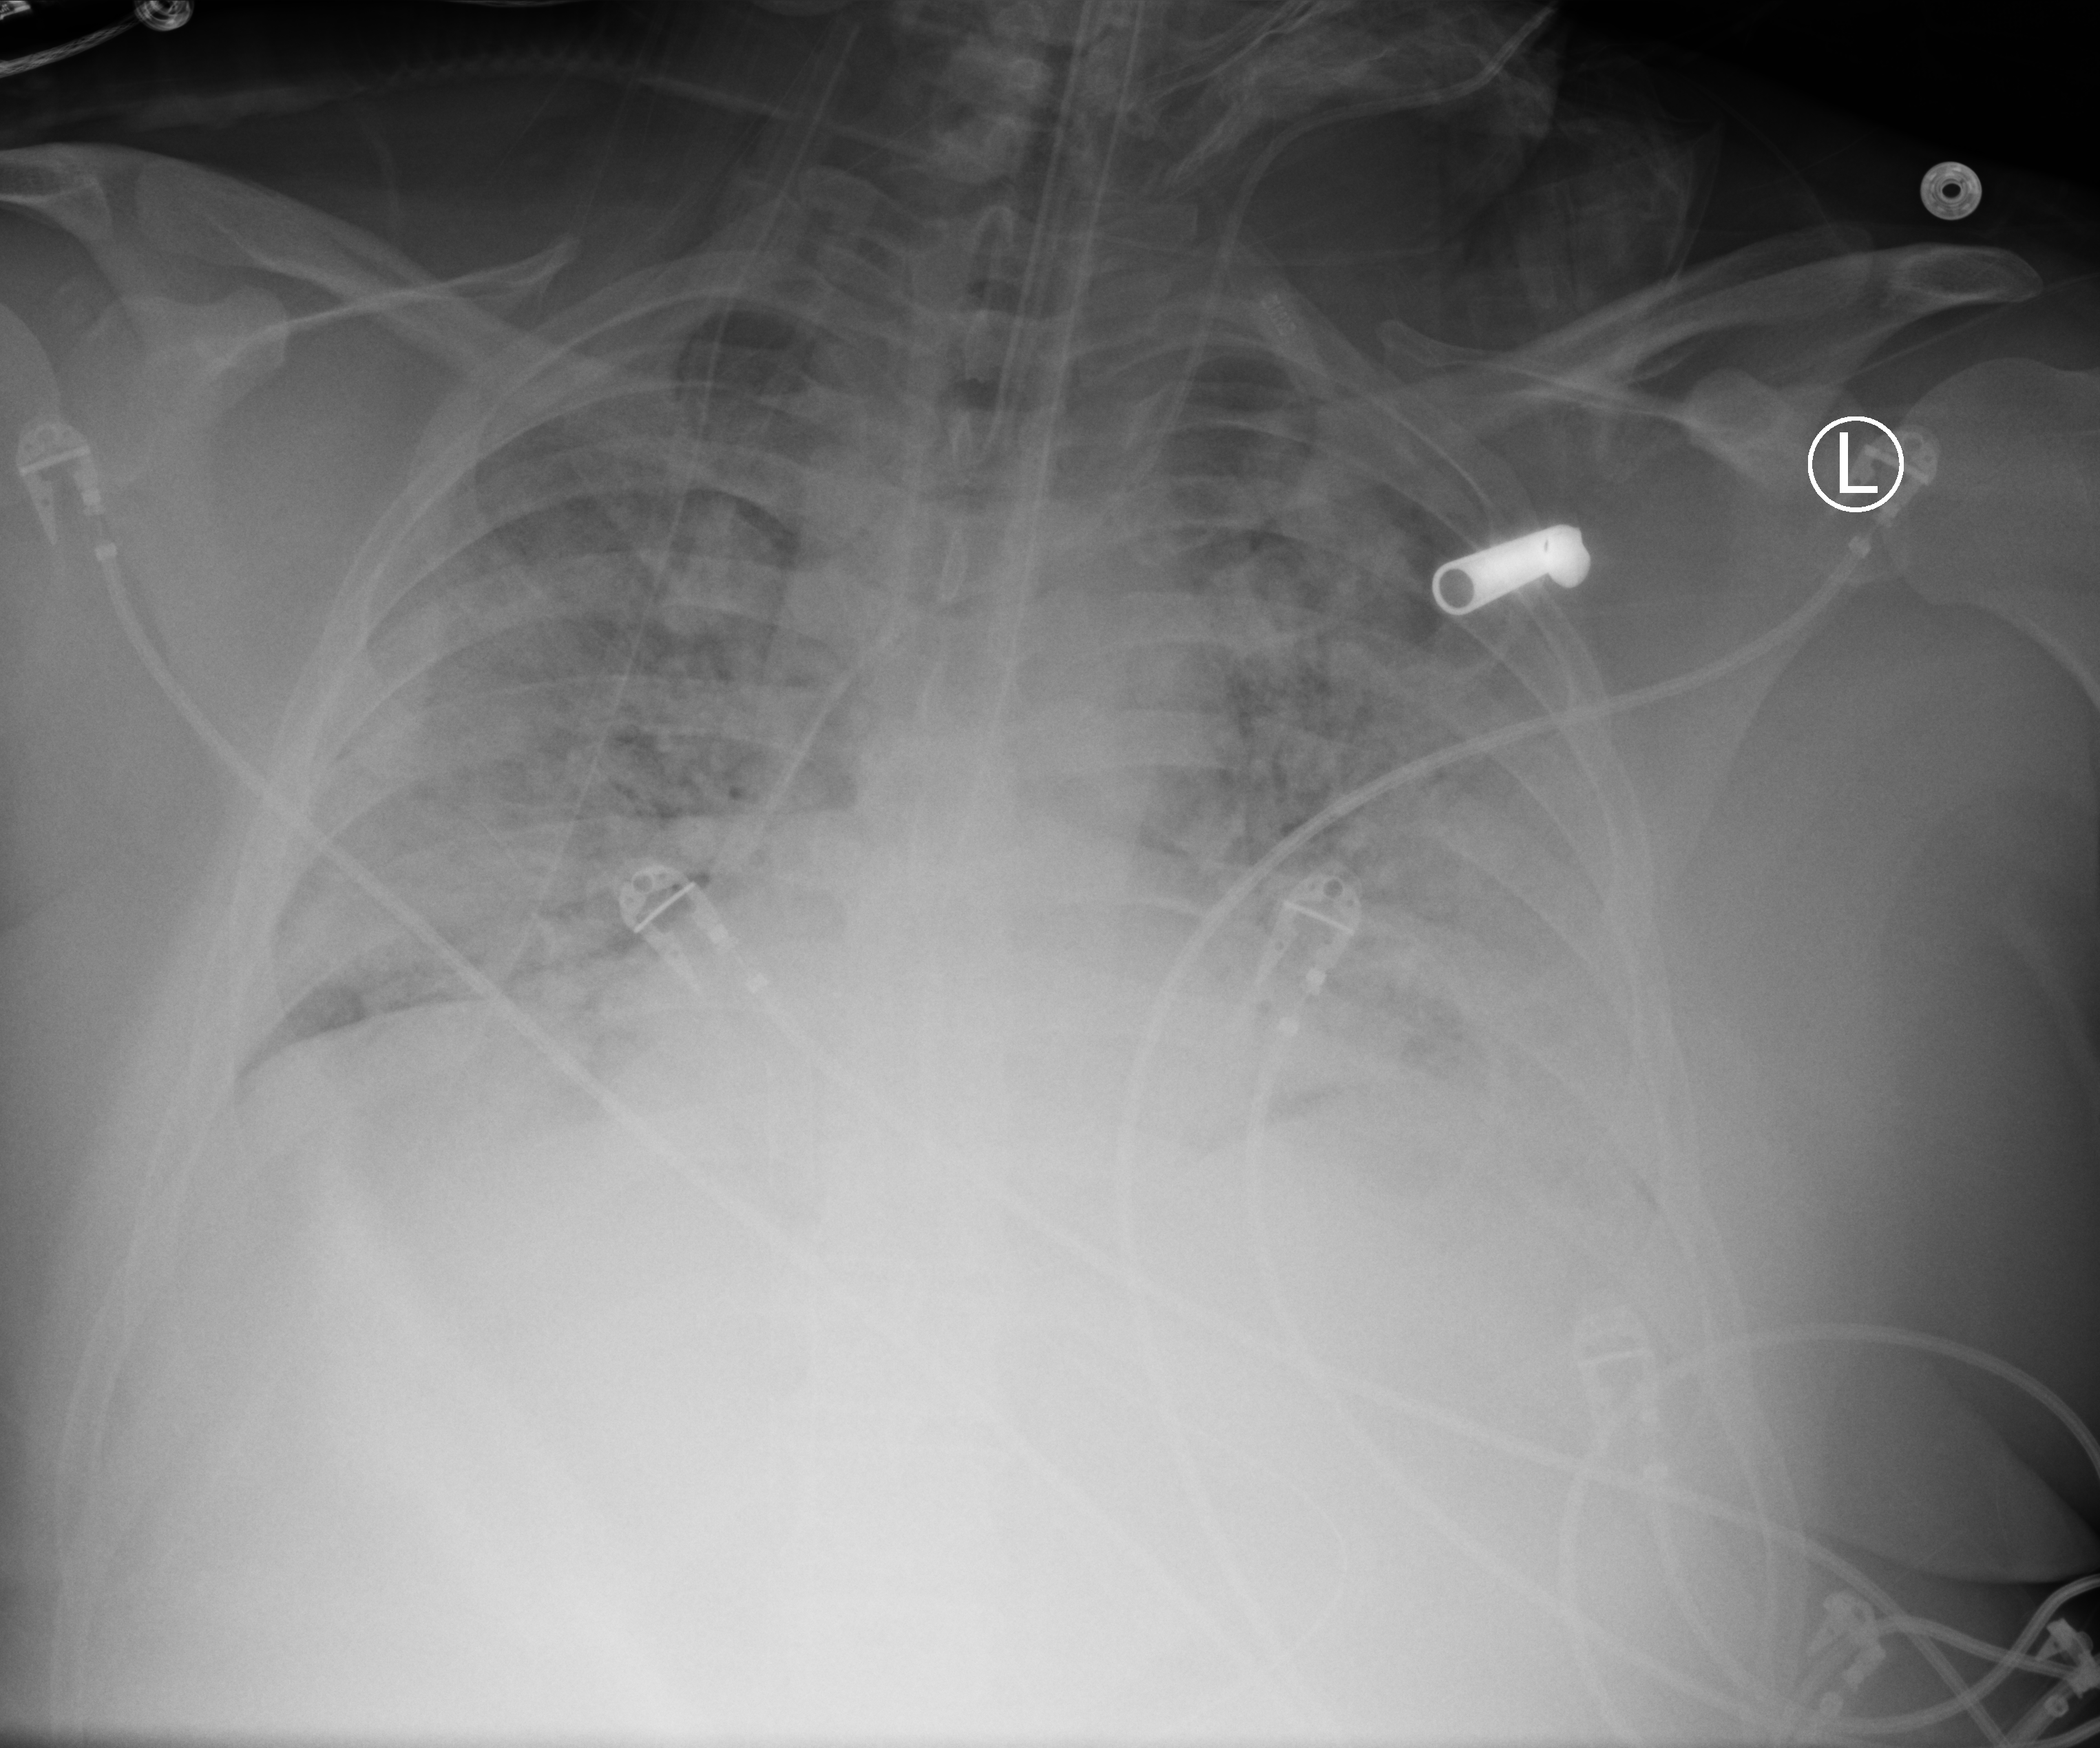
Portable chest radiograph; anteroposterior (AP) projection. Patient hospitalised with COVID-19, aged 18–59 years.
From the hospital-stay record, not from the radiograph (when in the stay this image was taken is not recorded):
- mechanically ventilated during this hospital stay: yes